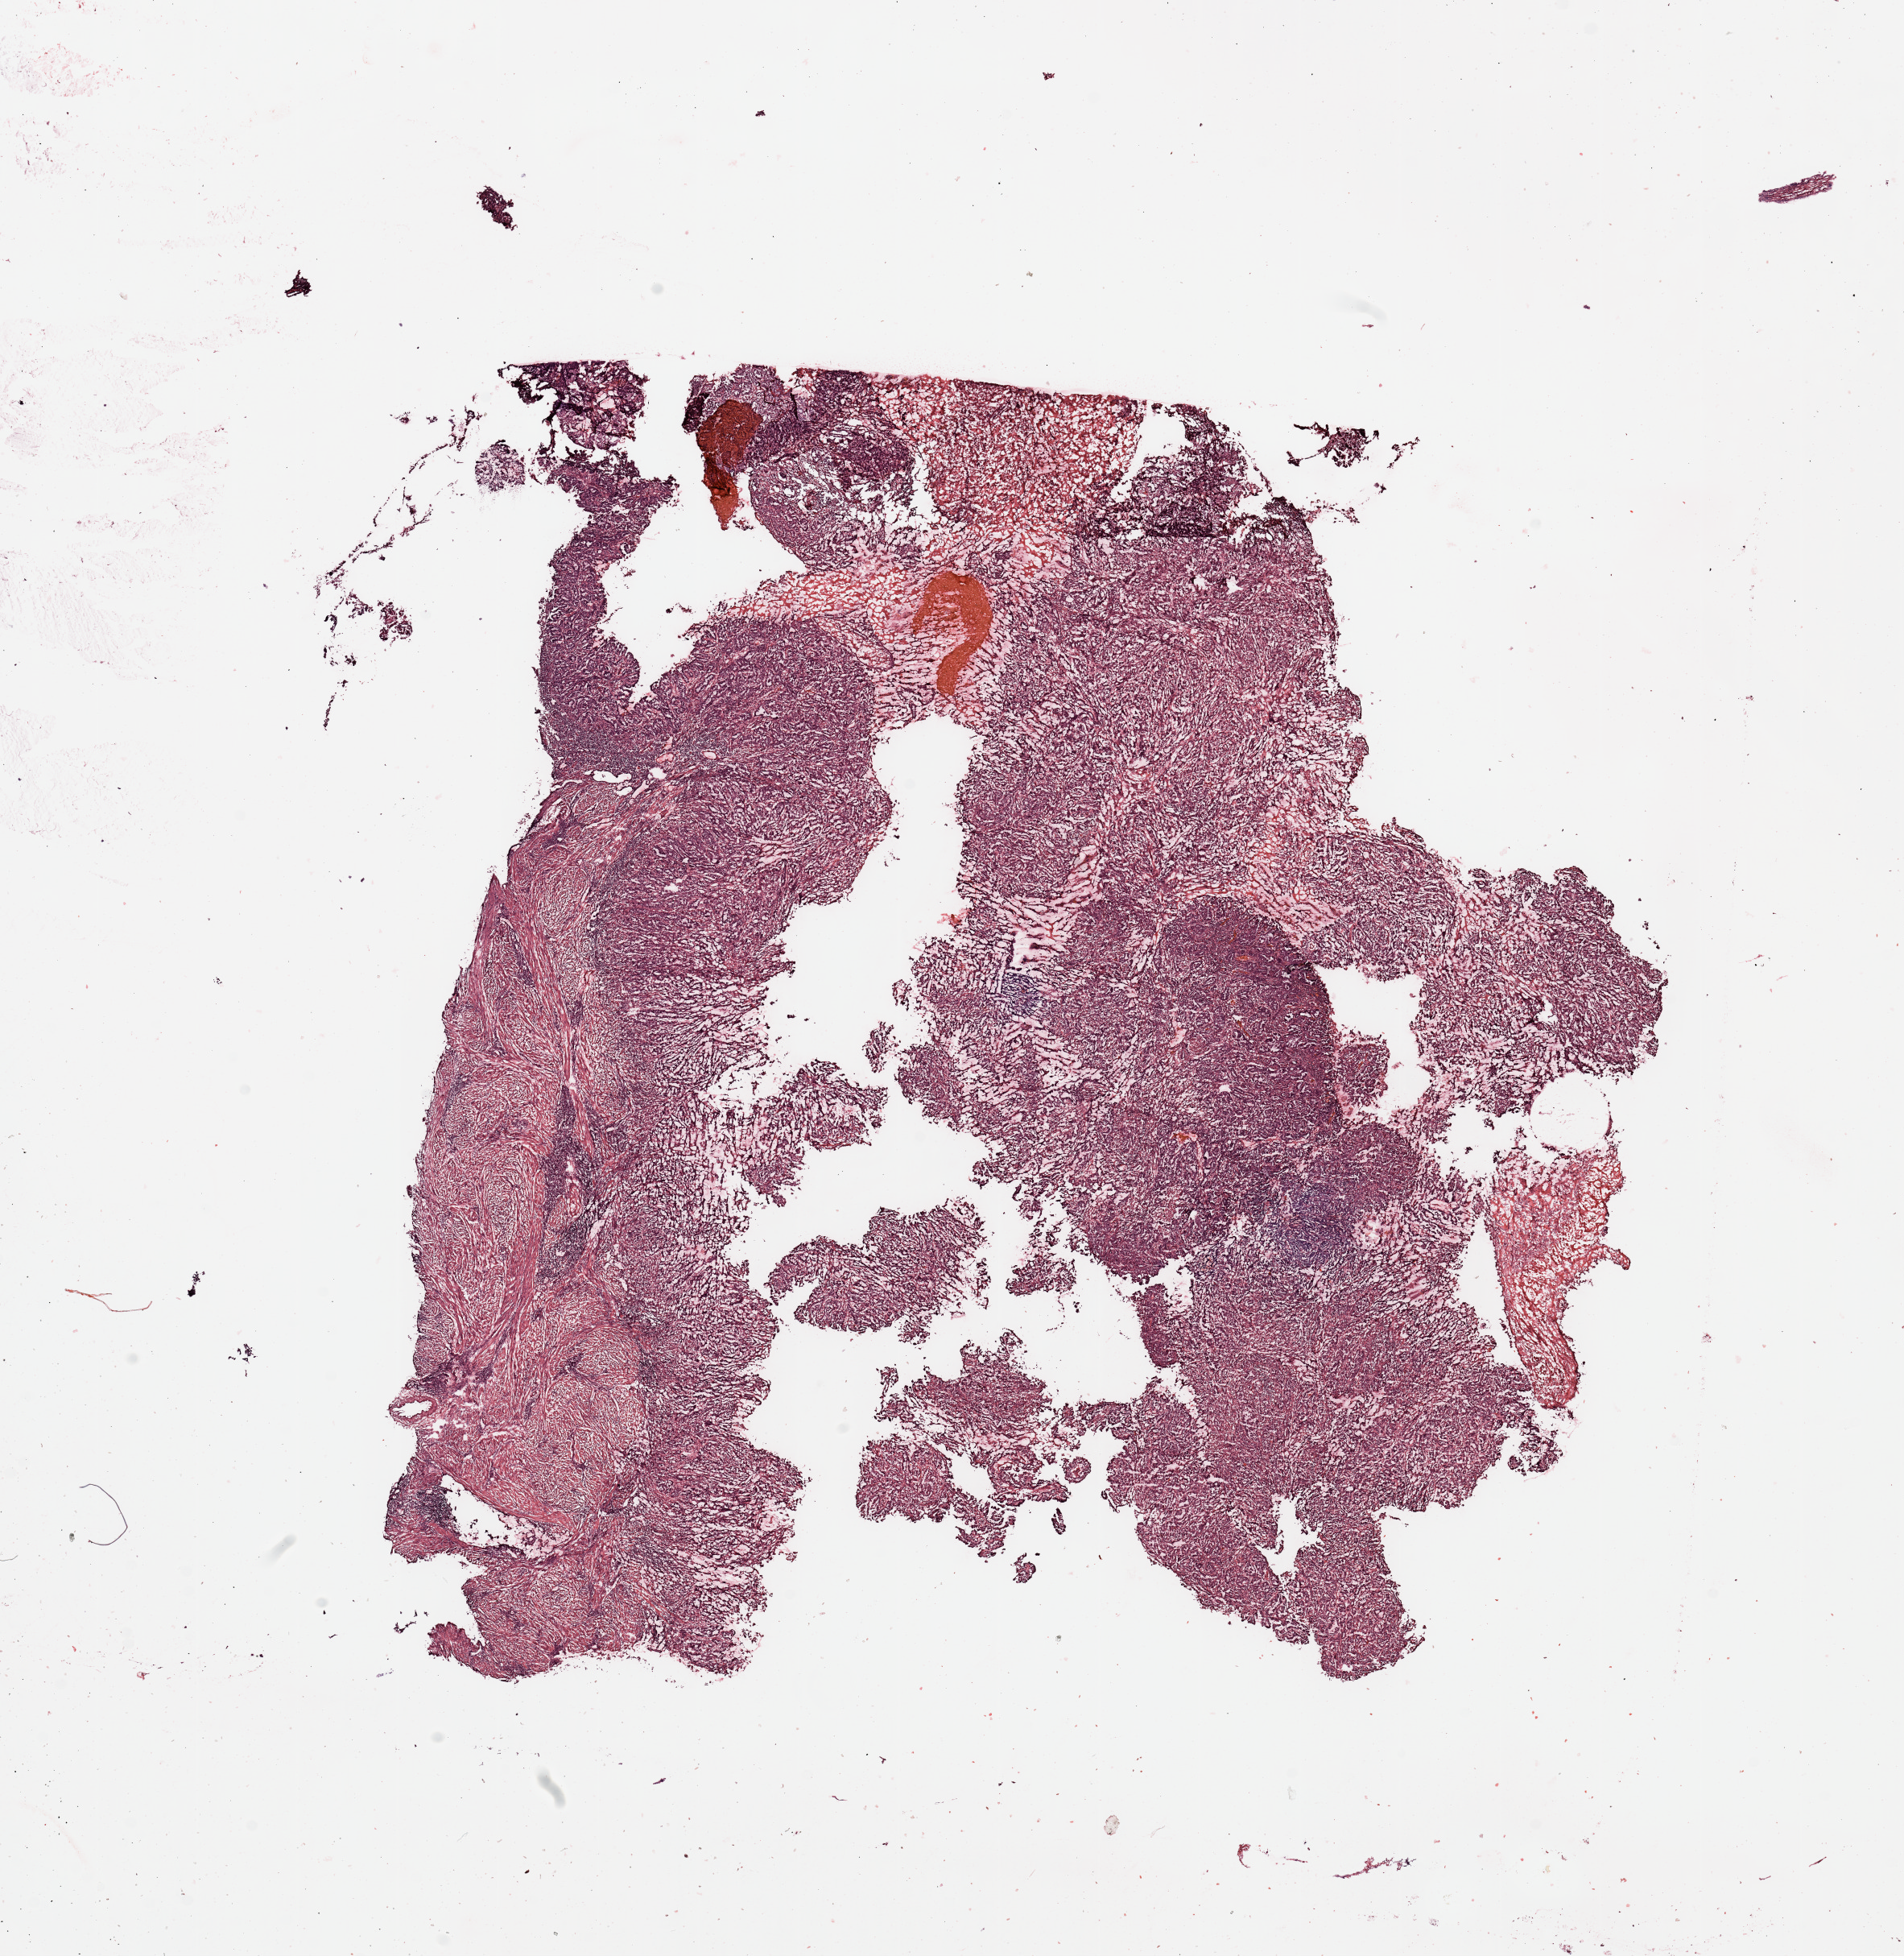
Whole-slide histology image, H&E — a low-resolution overview of the entire scanned area, about 18.7 x 19.2 mm (slide scanned at 20x); tumour tissue sample, uterus. Patient: female, age 57 years.
Diagnosis: Endometrioid adenocarcinoma, NOS.